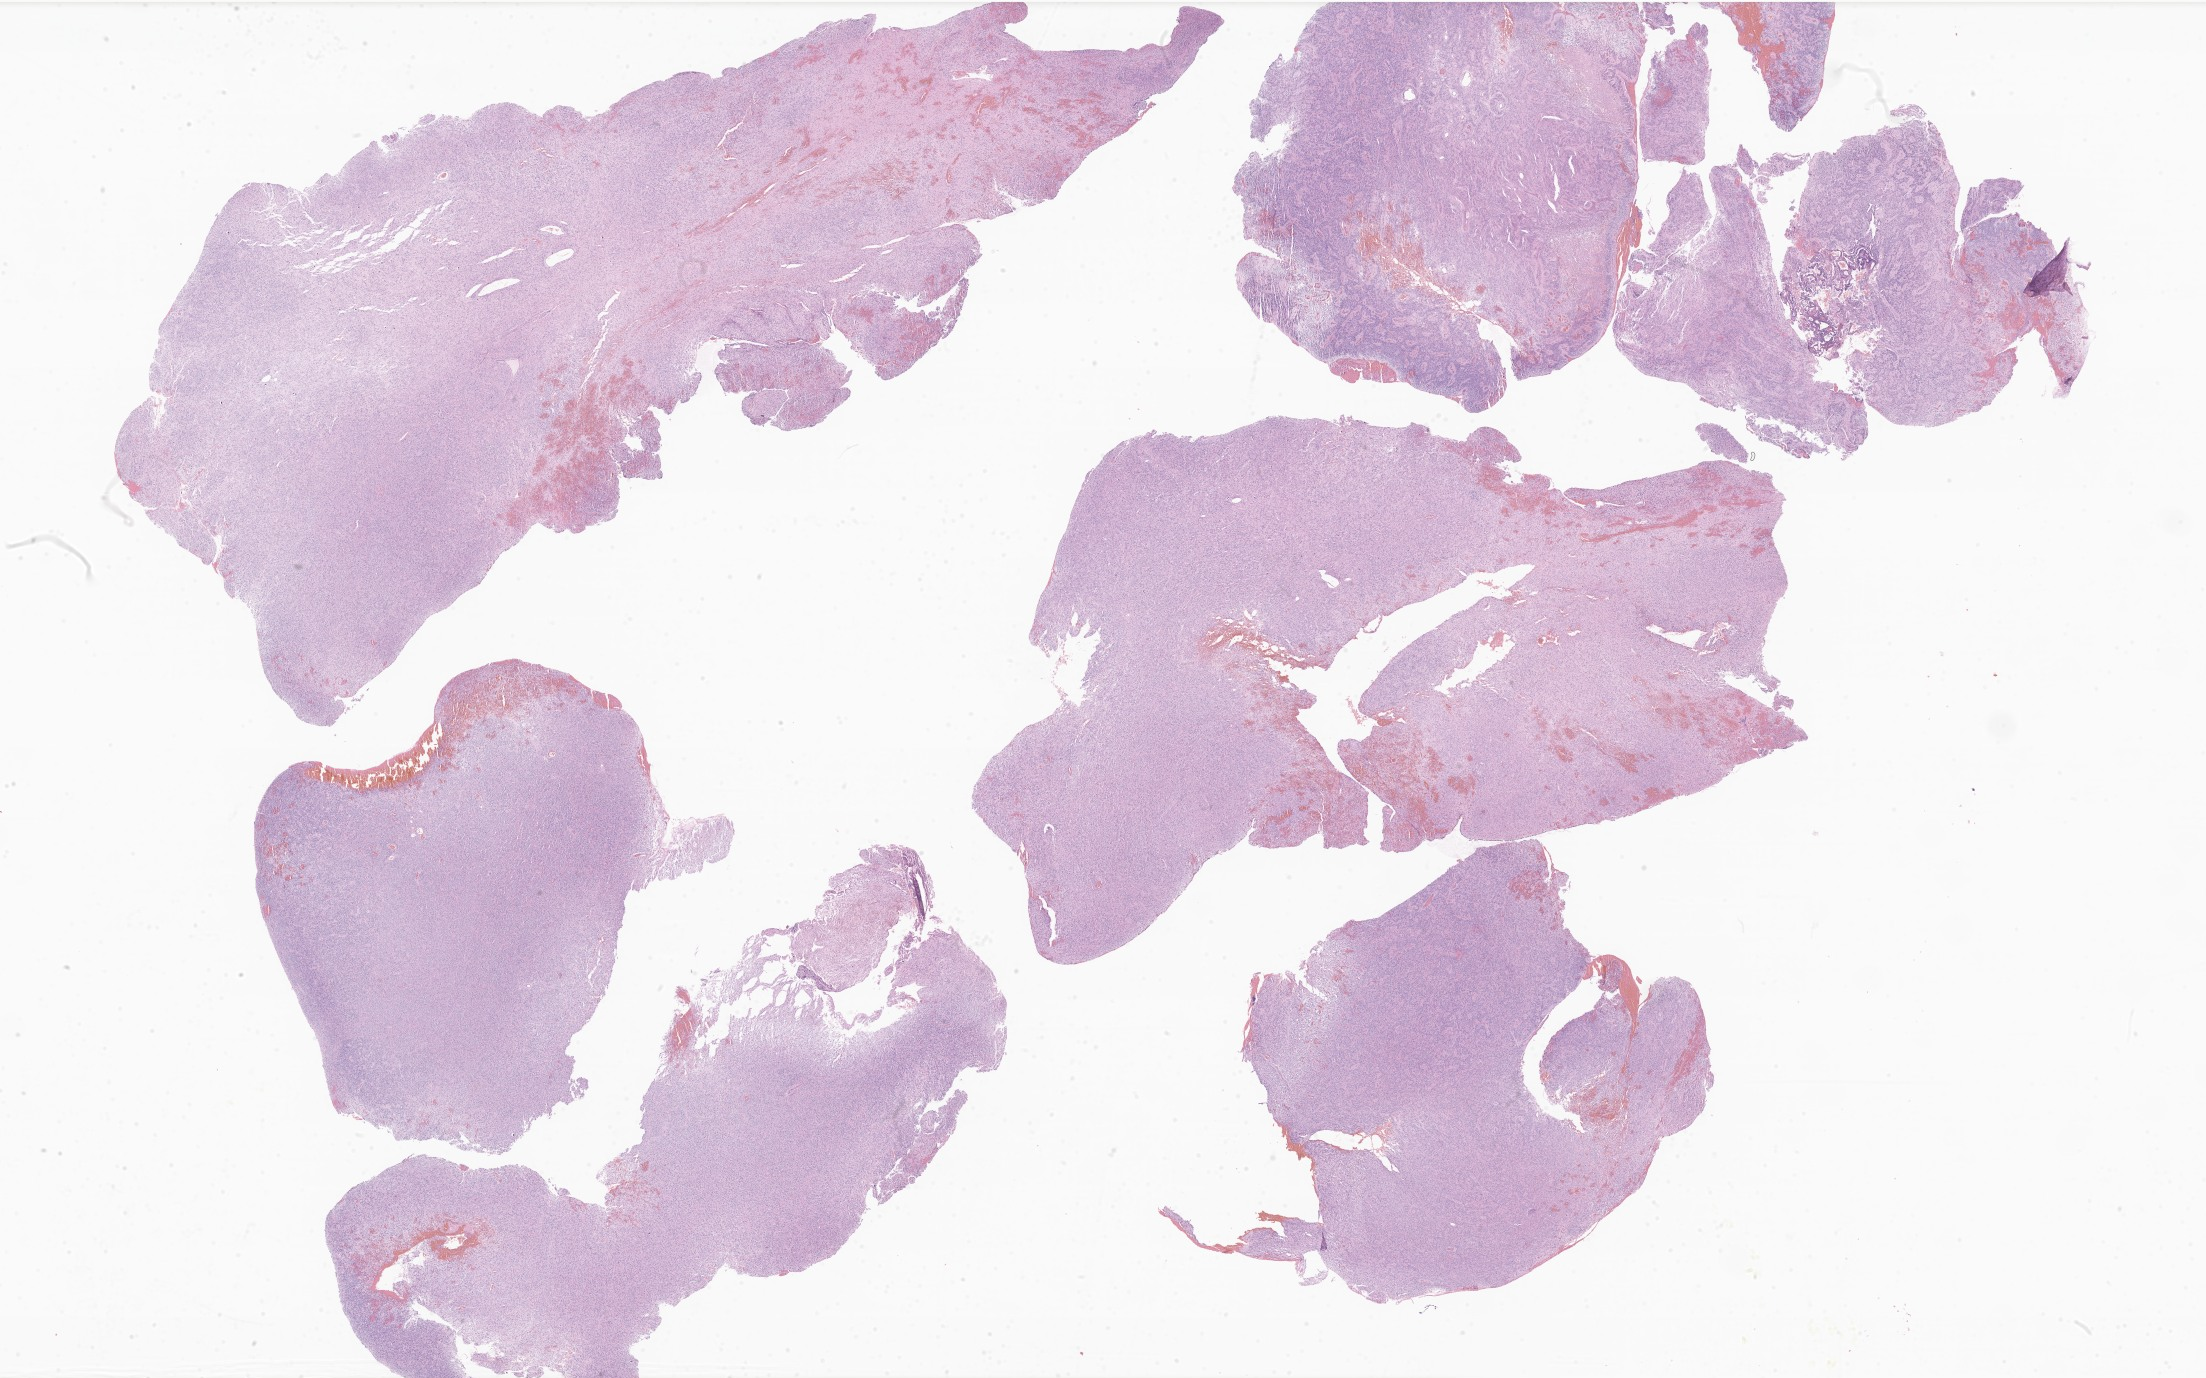
Hematoxylin and eosin (H&E) whole-slide image of tumor tissue from the brain — a low-resolution overview of the entire scanned area, about 37.2 x 23.2 mm. Male patient, age 463 days (about 1.3 years).
Specimen: FFPE section.